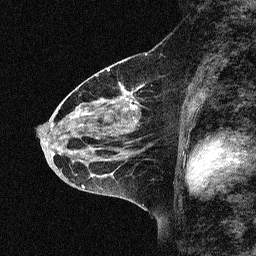
Breast MRI (dynamic contrast-enhanced), one sagittal slice; slice 33 of 64 in the series (ordered by position); dynamic contrast-enhanced study with each time point stored as its own series, time point 2 of 3 at this slice position (early post-contrast, ordered by acquisition time); 1.5 T; TE 4.5 ms, TR 11 ms; 2.06 mm slice thickness; 256 × 256 image matrix, field of view 200 × 200 mm. Female patient, age 46 years. From the clinical record (not read from this slice): setting: breast cancer imaged before/during neoadjuvant chemotherapy; receptor status: HER2-positive.
Annotated regions visible in this slice (semi-automatic segmentation, software-assisted and operator-edited):
- analysis volume of interest (the breast-tissue region the enhancement analysis was run in; not a lesion): bounding box <46,51,180,169> (left, top, right, bottom; pixels)
- tumour enhancement mask (voxels above the 90 % enhancement threshold inside the analysis volume of interest): <119,85,137,108>